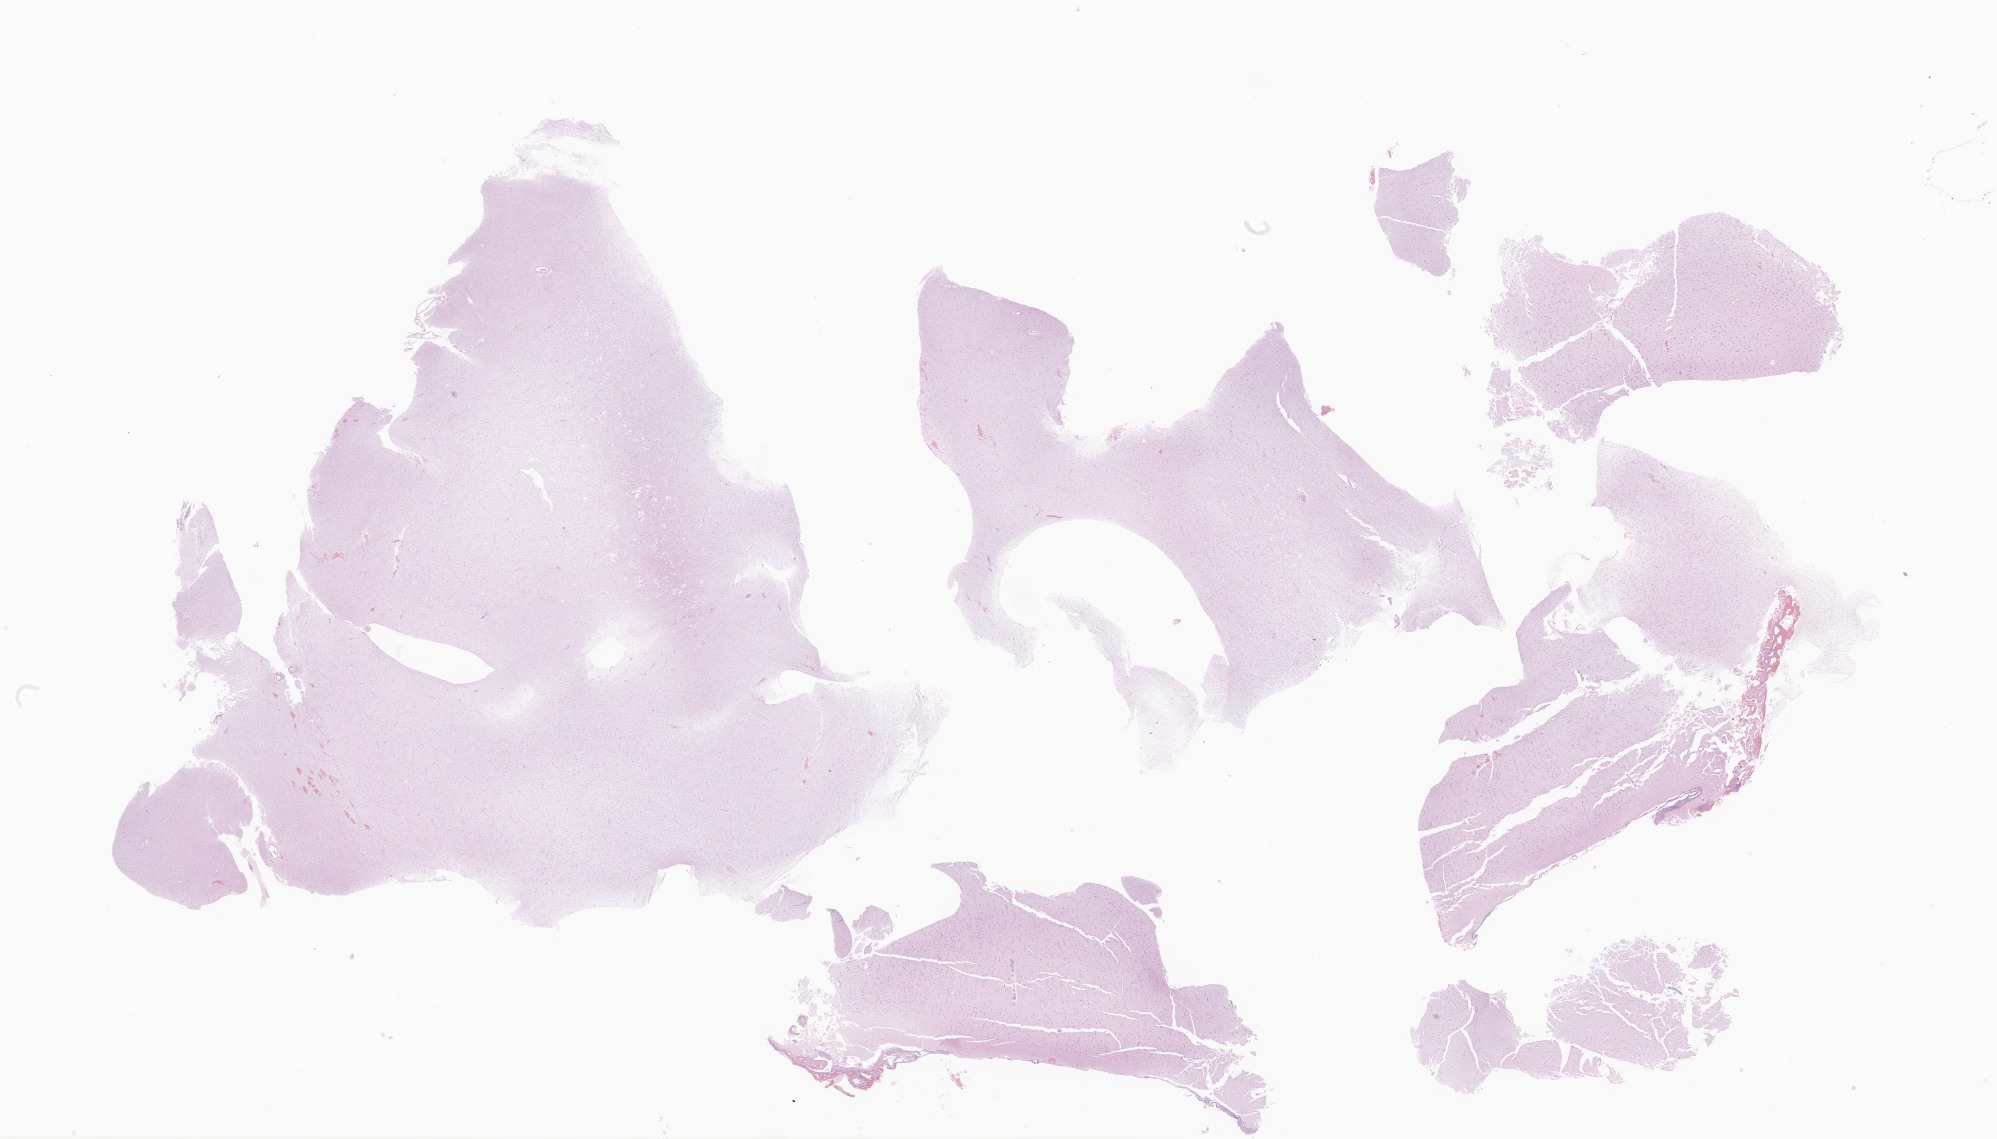
Whole-slide image, H&E stain of tumor tissue from the brain, a low-resolution overview of the entire scanned area, about 33.7 x 19.2 mm. FFPE section. Male patient, age 198 months (16 years 6 months).
- diagnosis (ICD-O-3 morphology term): Tumor cells, uncertain whether benign or malignant